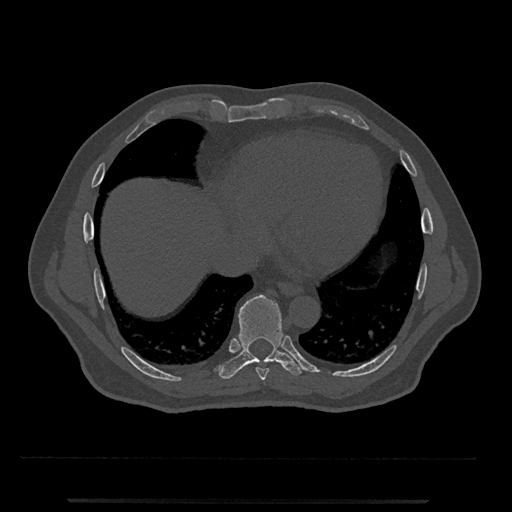
CT including the spine, one axial slice. Position 590 of 797 along the scan axis. 120 kVp. Bone window (W 1800 / L 400 HU). 0.5 mm slice thickness. 512 × 512 image matrix, field of view 419 × 419 mm. Male patient, age 63 years. From the clinical record (not read from this slice): primary cancer: prostate.
Structures marked on this image (semi-automatic segmentation, software-assisted and operator-edited):
- T8 vertebra: bounding box <256,367,270,380> (left, top, right, bottom; pixels)
- T9 vertebra: <219,295,305,379>